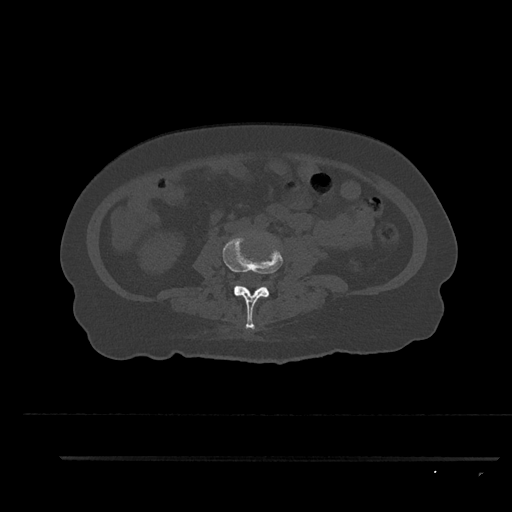
CT including the spine, one axial slice. Position 69 of 797 along the scan axis. Reconstruction kernel Br40s/3. 120 kVp. Bone window (W 1800 / L 400 HU). 0.5 mm slice thickness. 512 × 512 image matrix, field of view 408 × 408 mm. Patient: female, 44 years. From the clinical record (not read from this slice): primary cancer: renal; vertebrae with lytic lesions (as recorded): L1.
Structures marked on this image (semi-automatically segmented with operator editing):
- L3 vertebra: bounding box (x1, y1, x2, y2) in pixels: (222, 234, 283, 330)
- L4 vertebra: (271, 288, 274, 291)